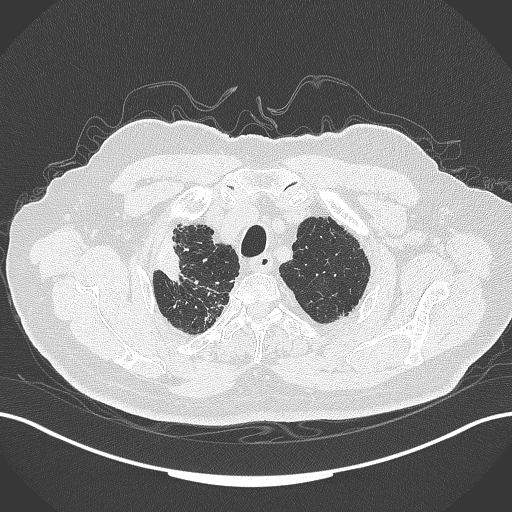
Chest CT, one axial slice. Slice 313 of 389 in the series (ordered by position). Reconstruction kernel B70f. Lung window (W 1500 / L -600 HU). 1 mm slice thickness. 512 × 512 image matrix, field of view 400 × 400 mm. Male patient, age 72 years. From the clinical record (not read from this slice): clinical TNM (as recorded): T1a N0 M0.
Outlined on this slice (bounding box drawn by a radiologist):
- lung tumour (recorded histology: squamous cell carcinoma): box from (x=151, y=232) to (x=184, y=278) px